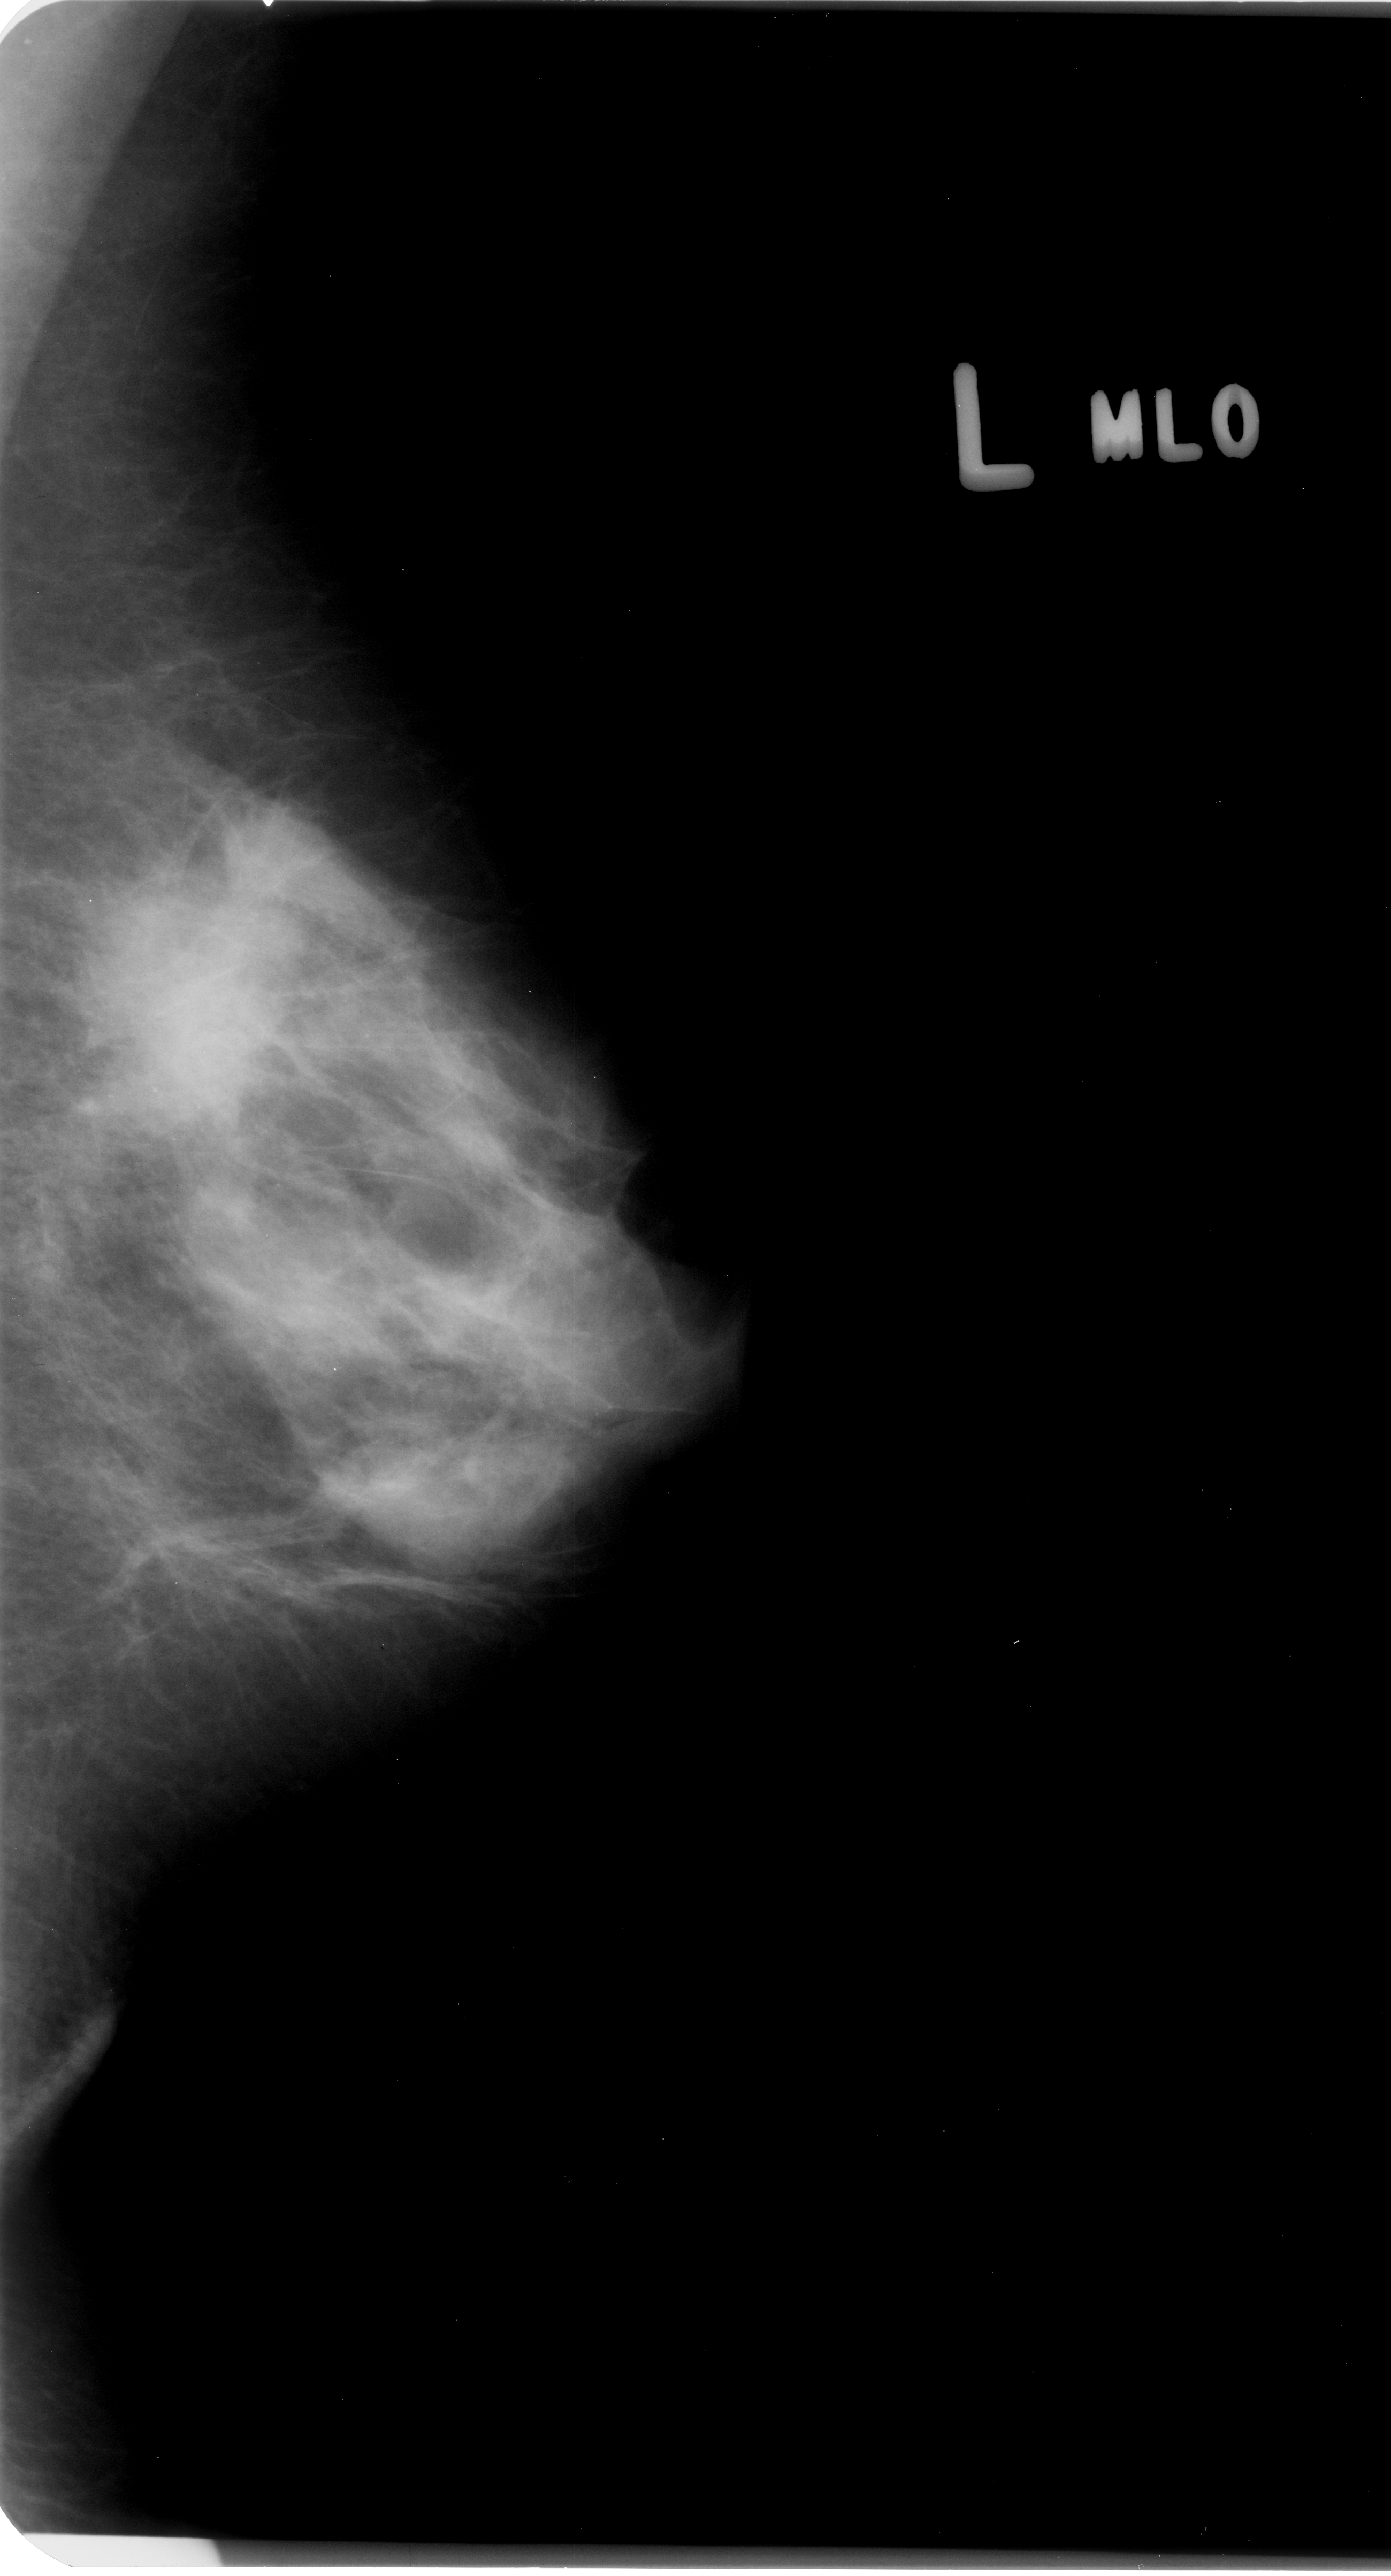
Mammogram (digitized film). Left breast. Mediolateral oblique (MLO) view. 1391 × 2576 image matrix.
Marked abnormalities (boxes around the expert regions of interest):
- Finding 1 of 2: calcifications, morphology amorphous / round and regular, distribution clustered; BI-RADS assessment category 4; pathology result (as recorded, not read from the image): malignant: bounding box (x1, y1, x2, y2) in pixels: (85, 1086, 108, 1118)
- Finding 2 of 2: calcifications, morphology amorphous / round and regular, distribution clustered; BI-RADS assessment category 4; pathology result (as recorded, not read from the image): malignant: (145, 1069, 172, 1109)